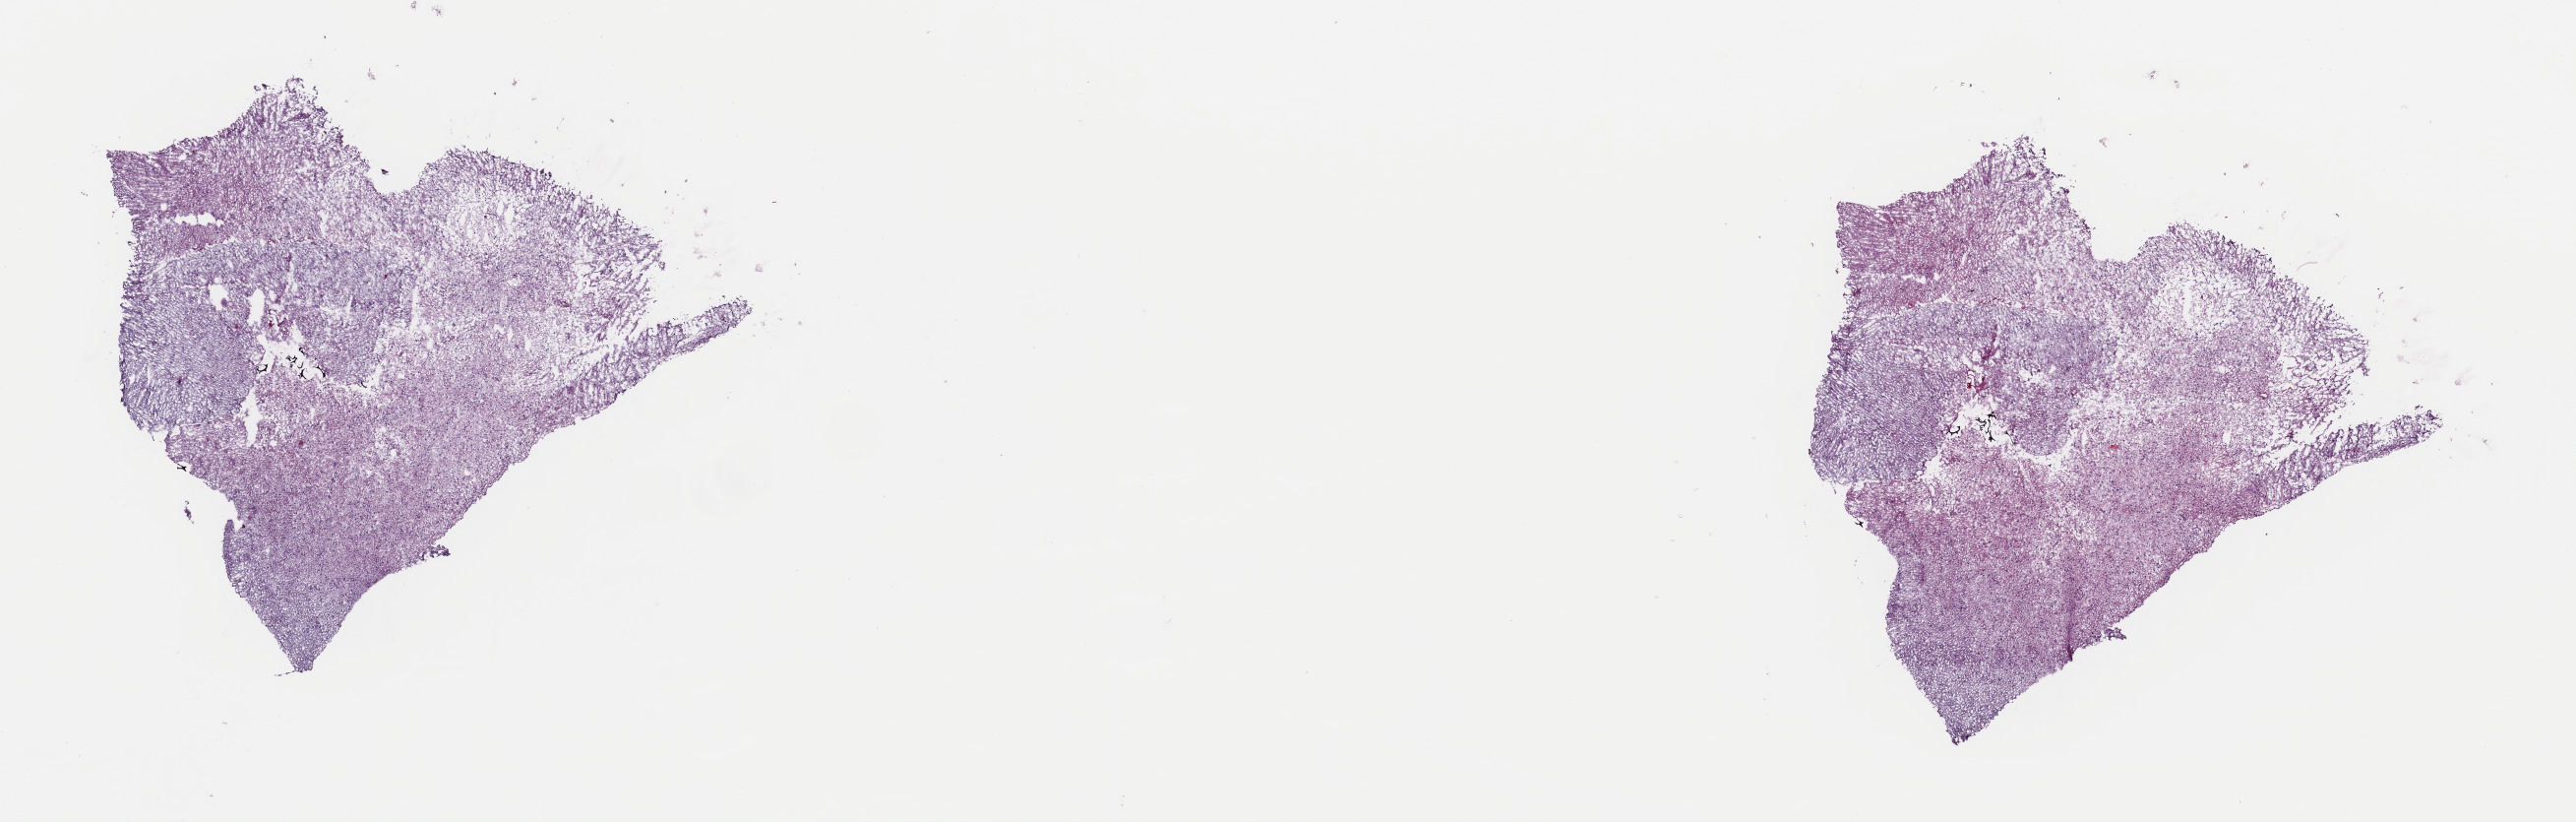
Digitized H&E tissue section (whole slide) — low-resolution overview of the scanned area, about 20.7 x 6.6 mm (acquisition: 40x scan); frozen section; sample: primary tumour, brain. Male patient; age at initial diagnosis 47 years. Pathologist review of this section (percent, as recorded): tumour cells 45%, tumour nuclei 70%.
Pathologic diagnosis: Mixed glioma (cerebrum).